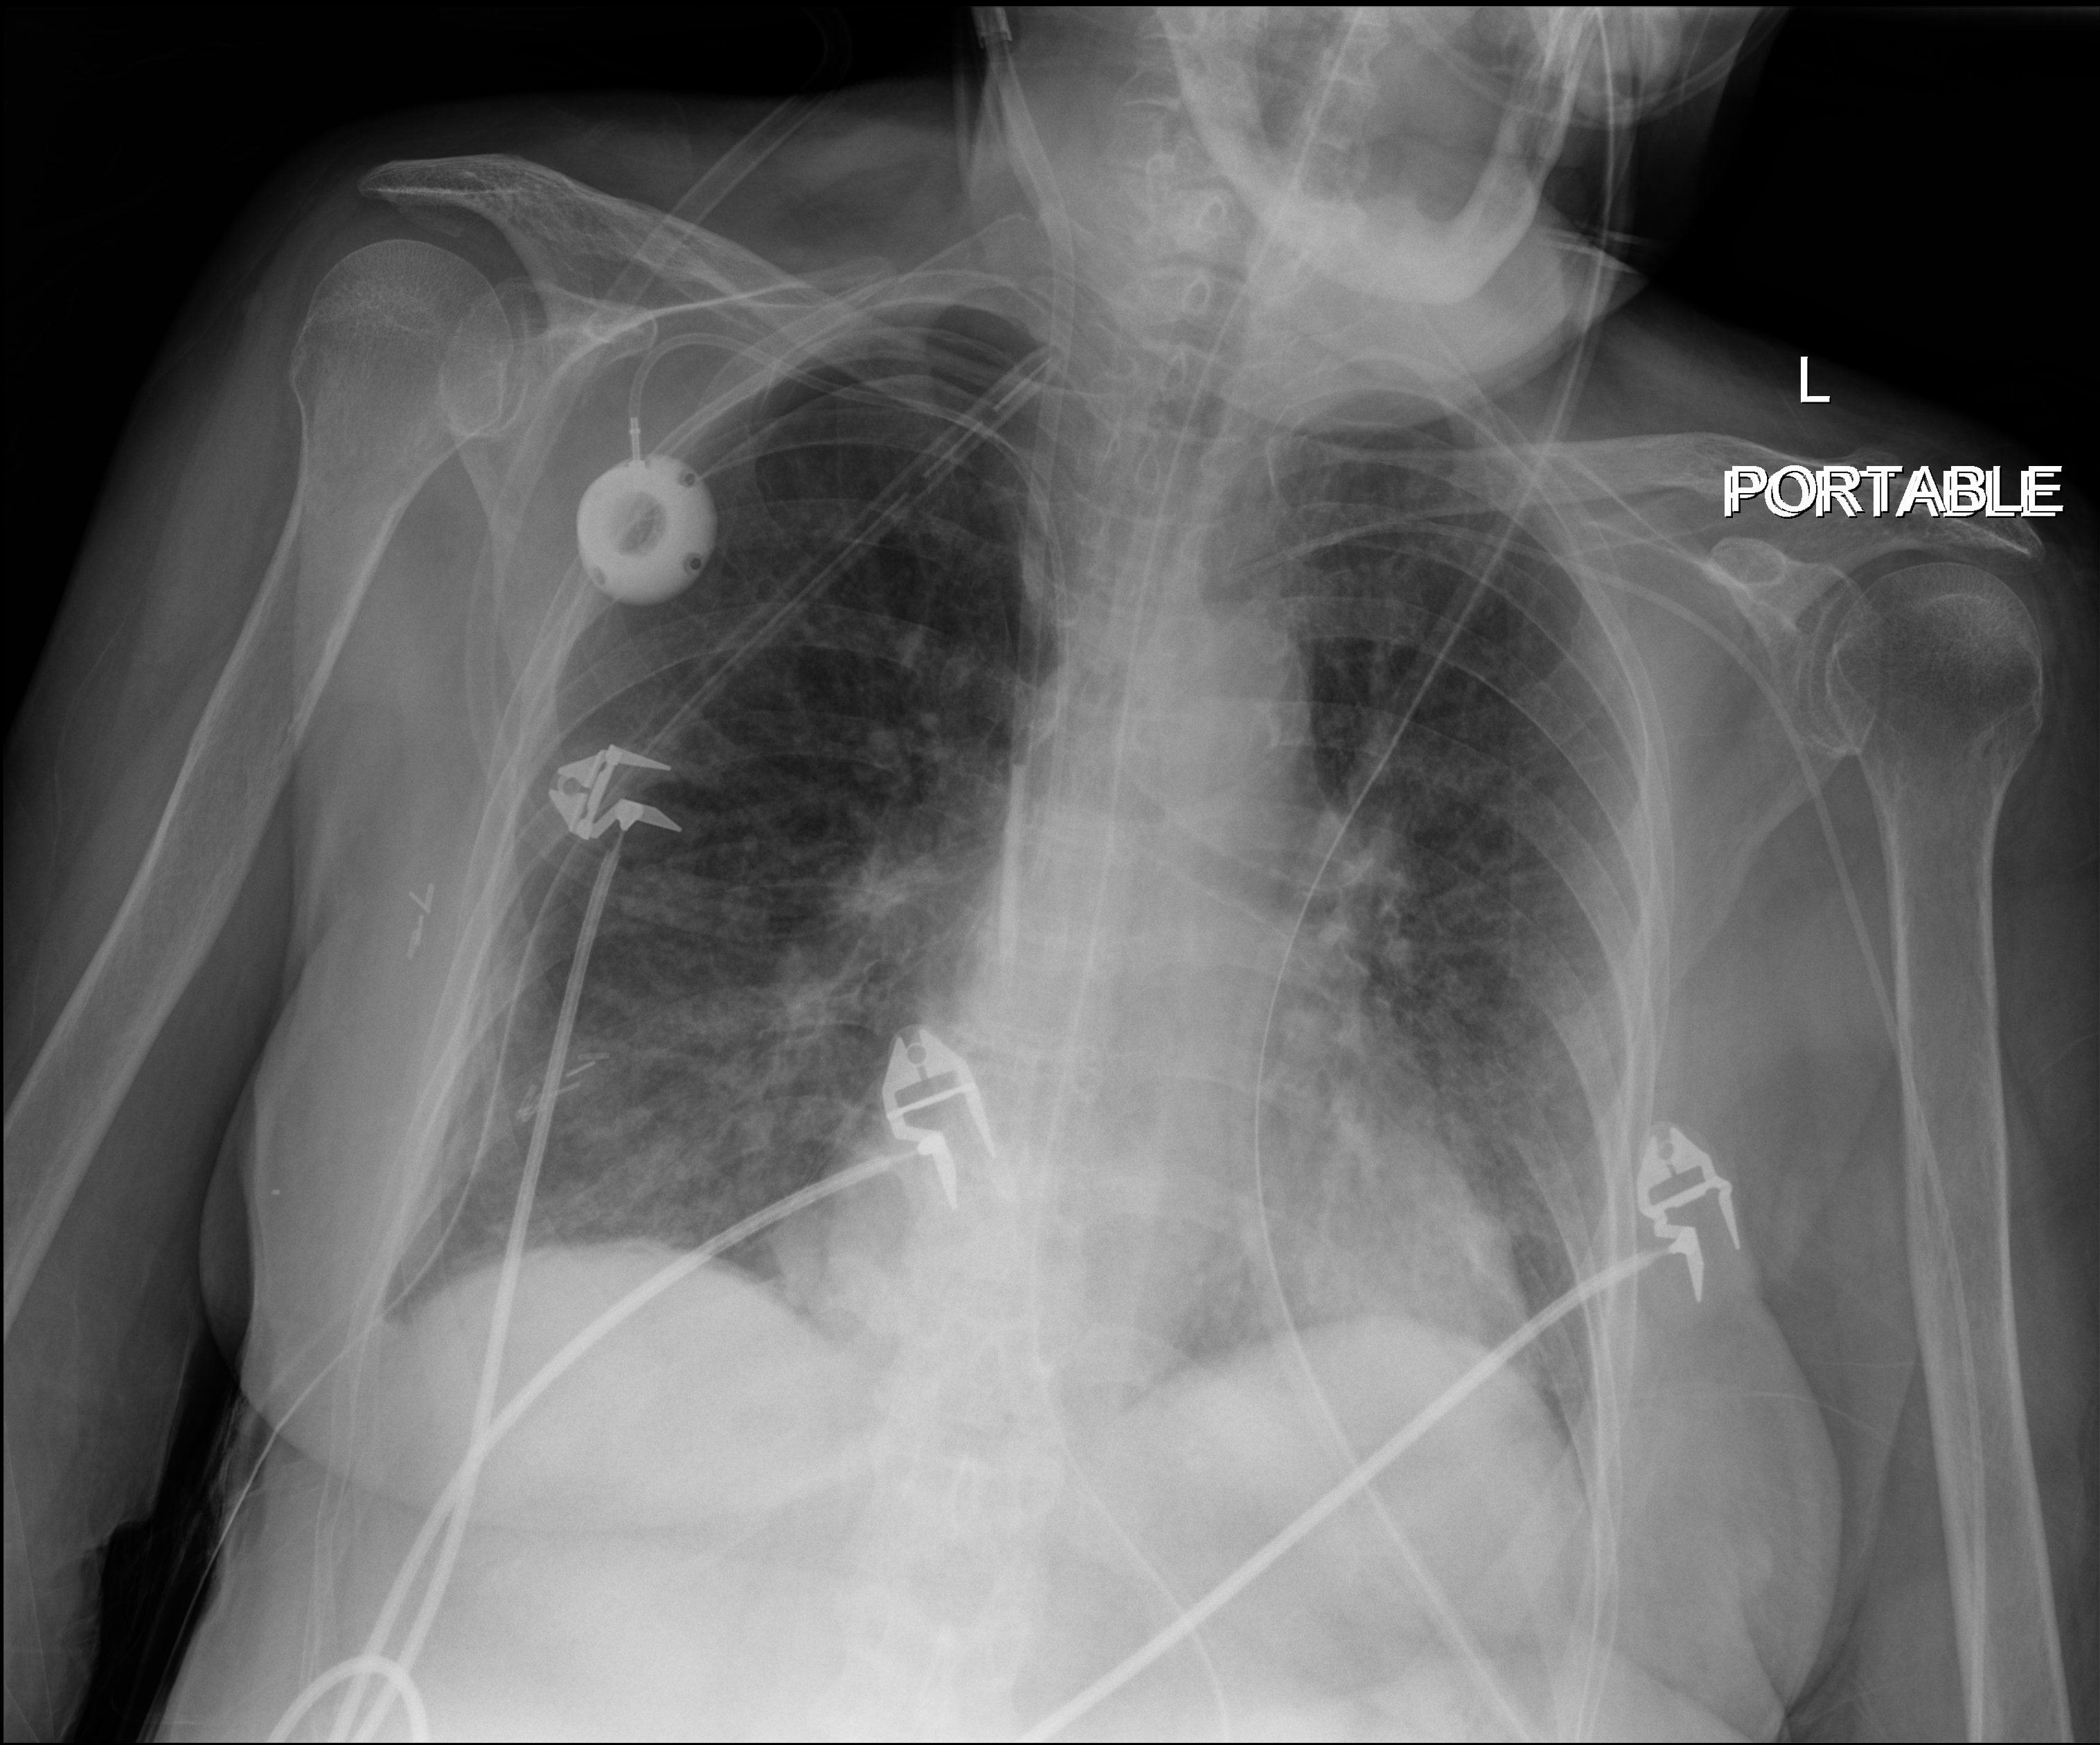
Chest X-ray, anteroposterior (AP) projection. Patient hospitalised with COVID-19; female, aged 60–74 years.
Admission-level facts for this patient (not findings on this image; timing relative to this image not recorded): COPD (admission record): no.